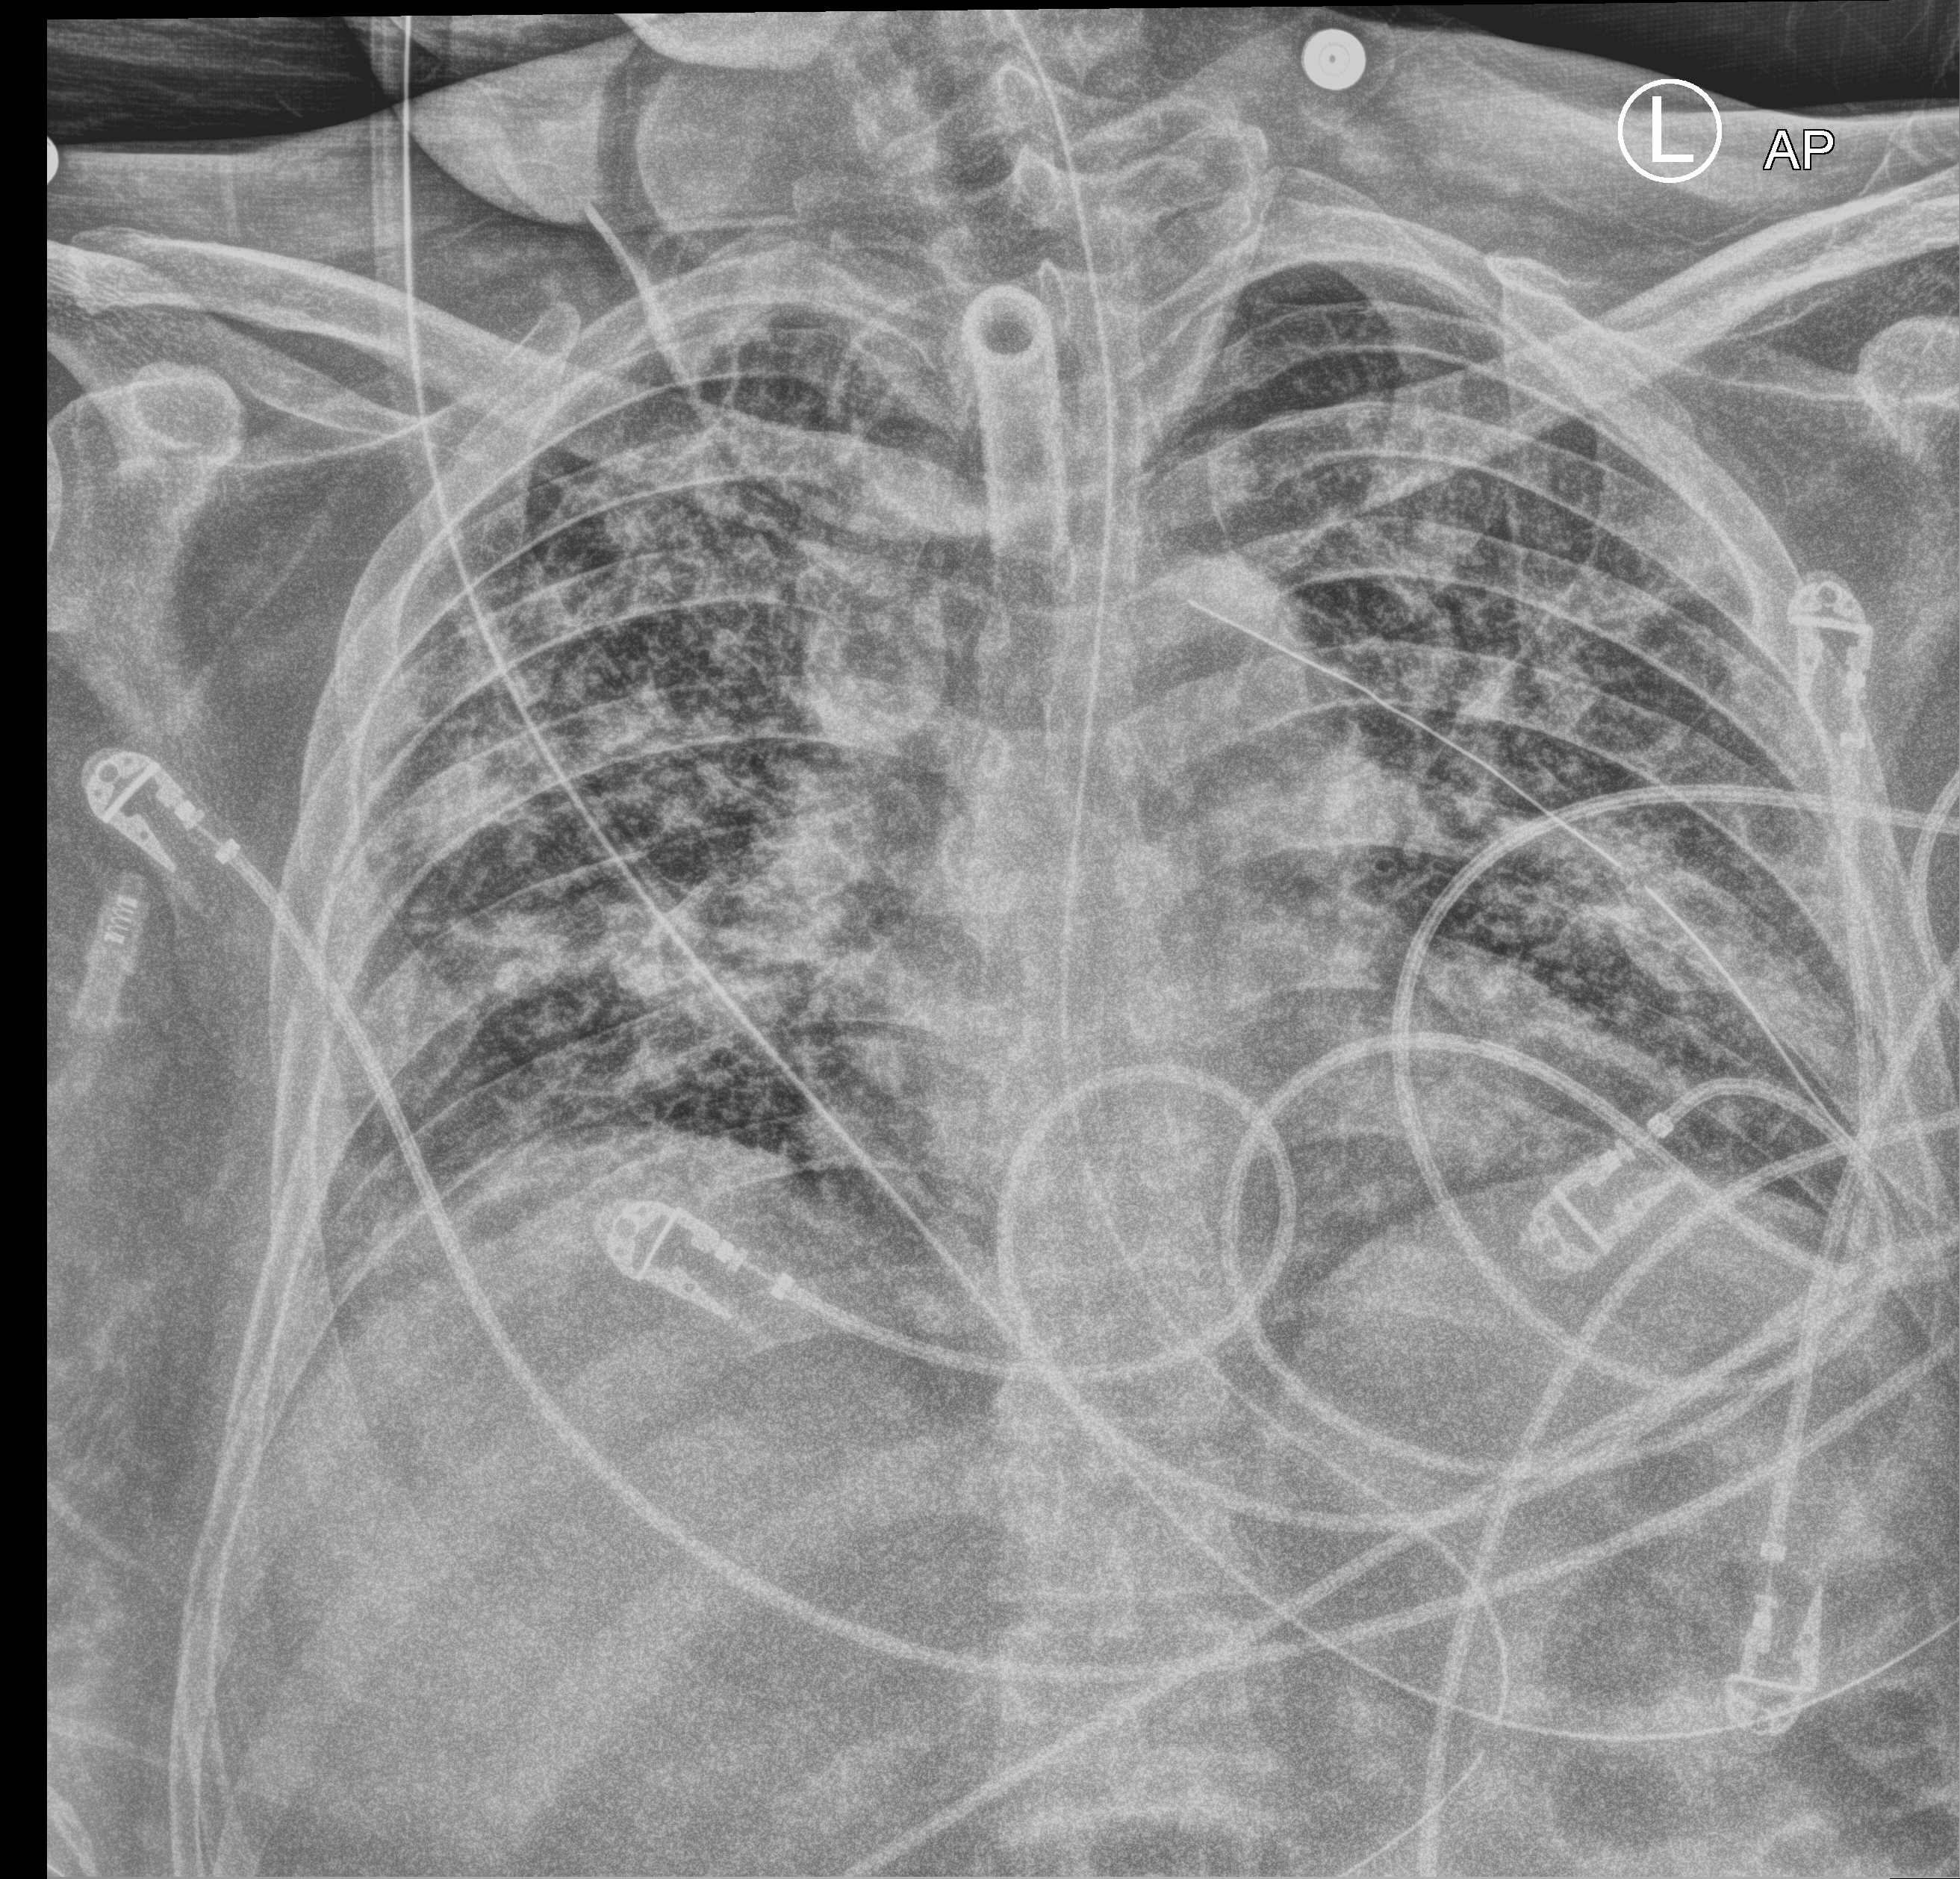
Chest X-ray (portable), anteroposterior (AP) projection. Male patient hospitalised with COVID-19, age 18–59 years.
Admission-level facts for this patient (not findings on this image; timing relative to this image not recorded):
- mechanically ventilated during this hospital stay: yes